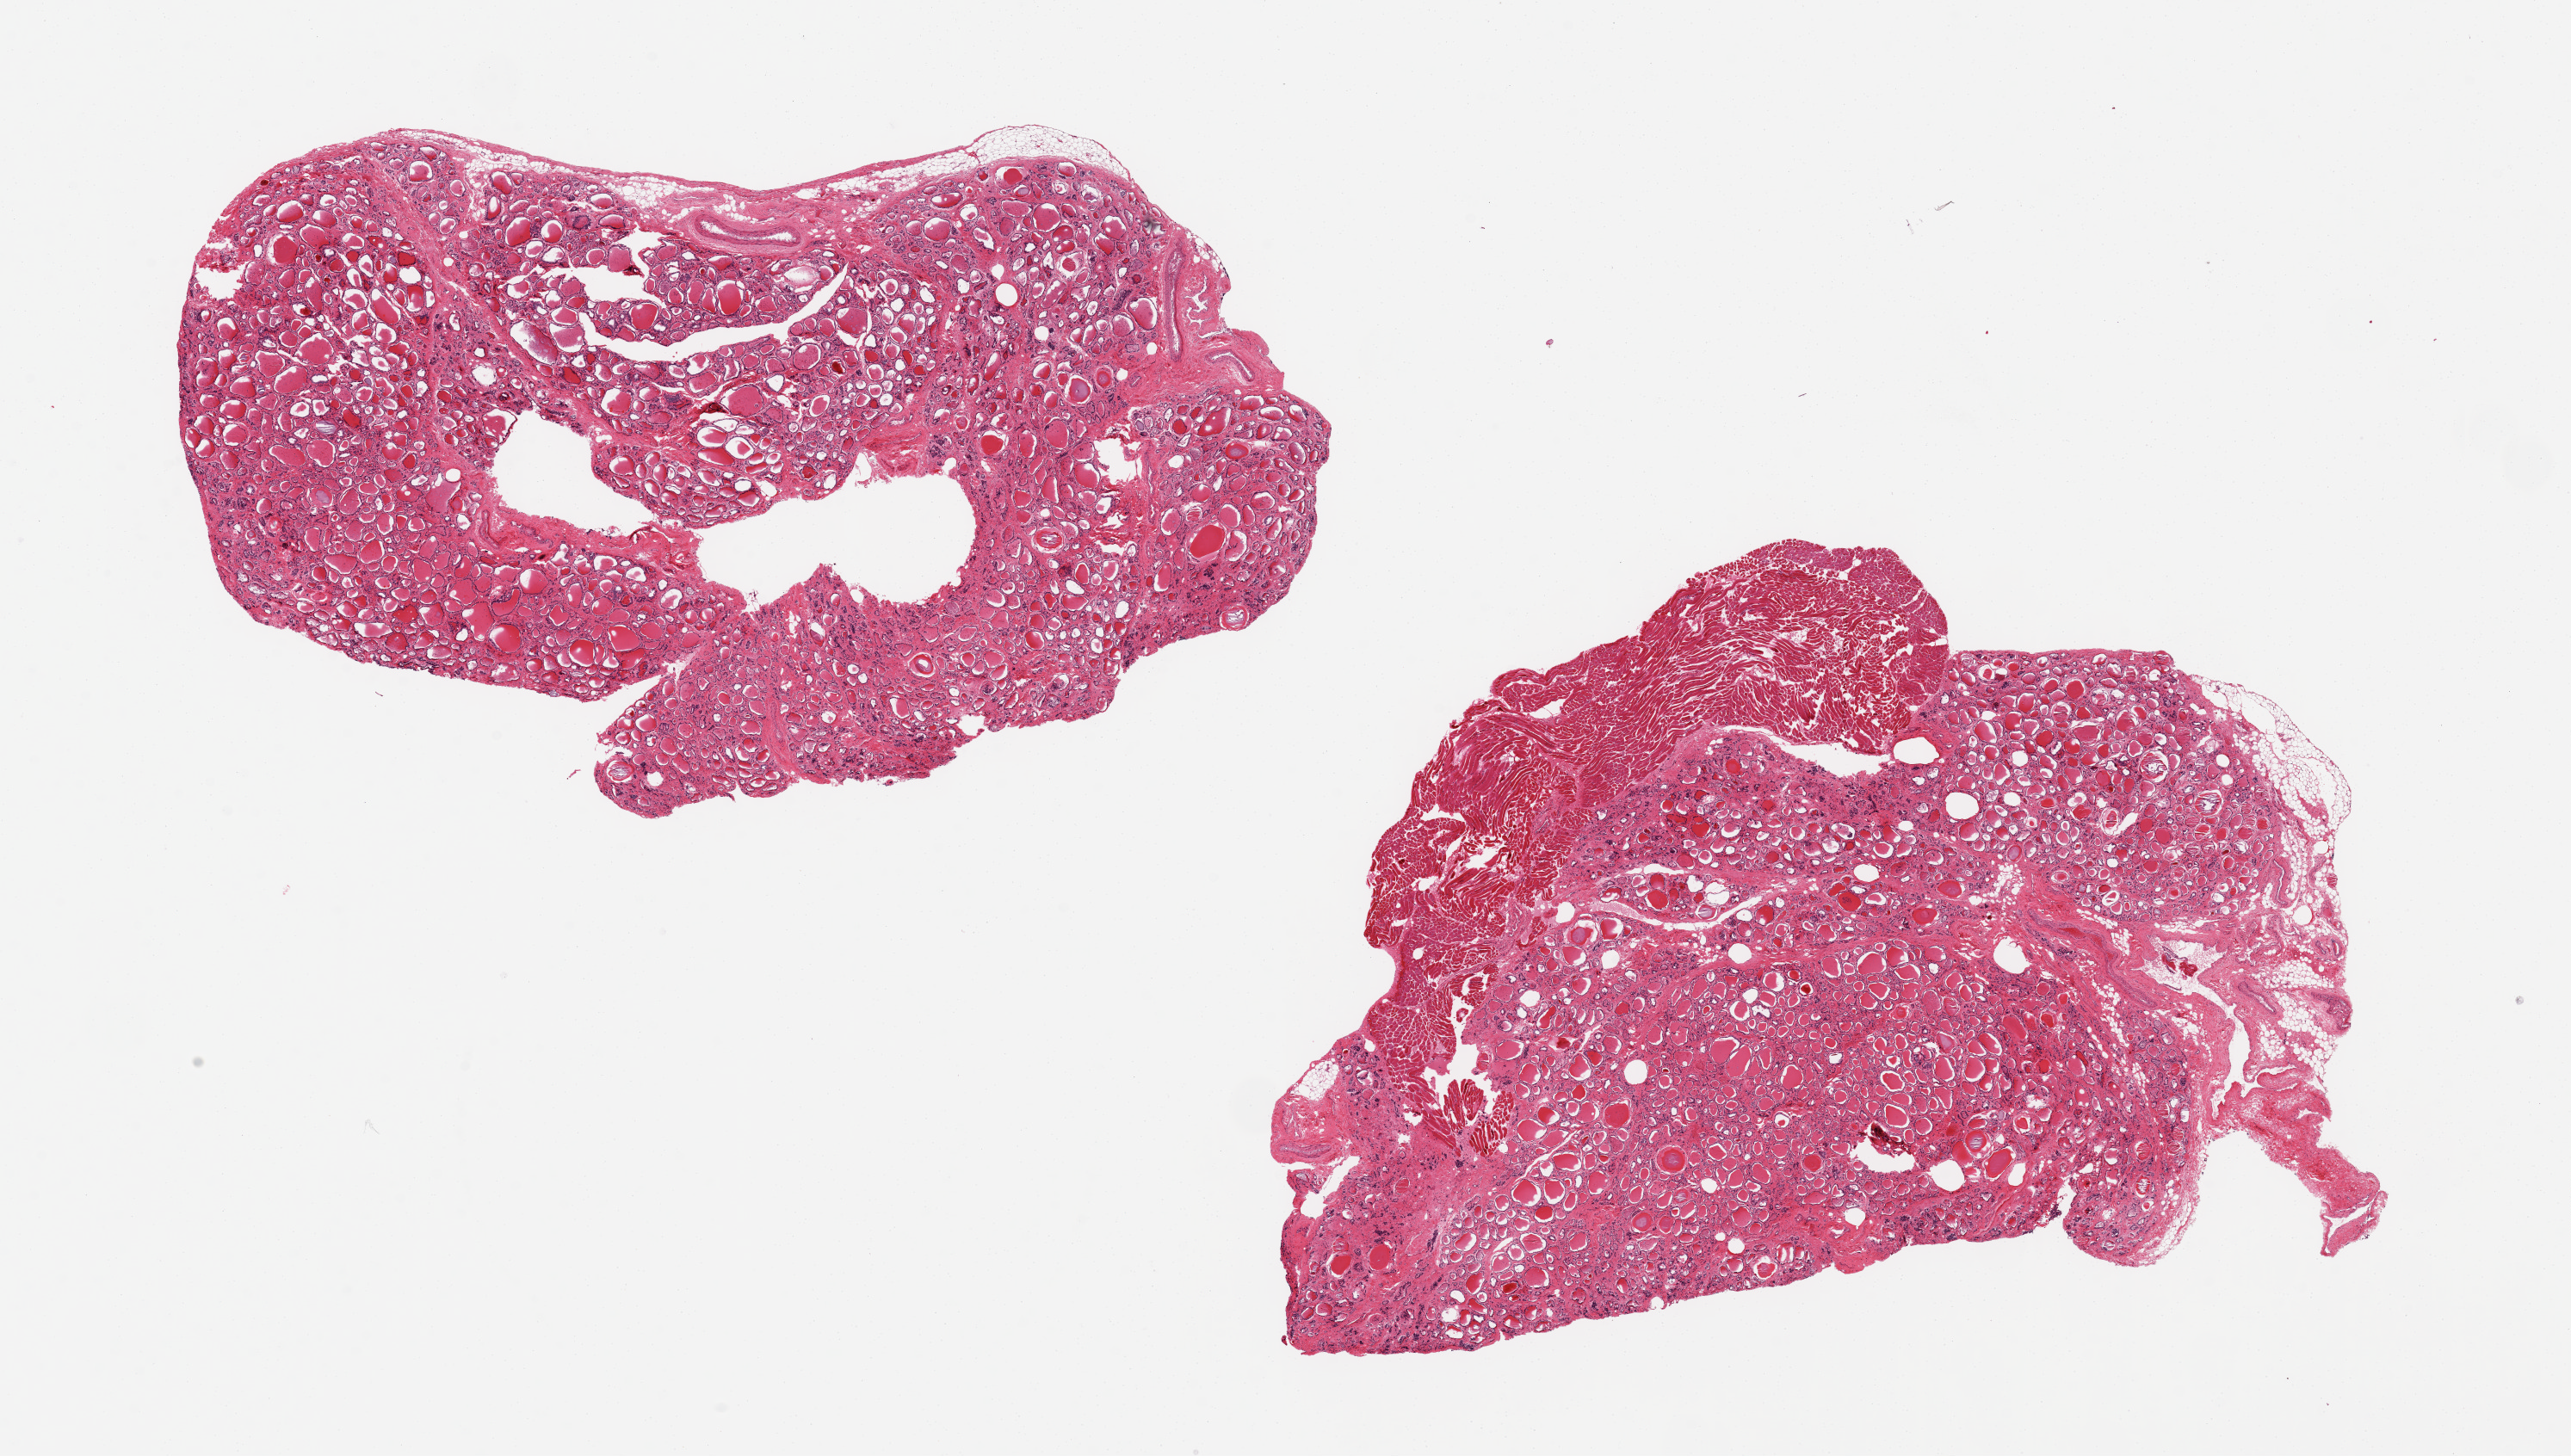
Digitized haematoxylin and eosin-stained section, shown as a low-resolution overview of the whole scanned area (about 23.6 x 13.4 mm, slide scanned at 20x); PAXgene-fixed paraffin-embedded (PFPE) section; sampled site (target tissue): thyroid; donor tissue sample. Donor sex: female.
Reviewer comment on this tissue sample: 2 pieces, 10x6 & 10x7 mm; ~25% skeletal muscle at edge of 1 piece.